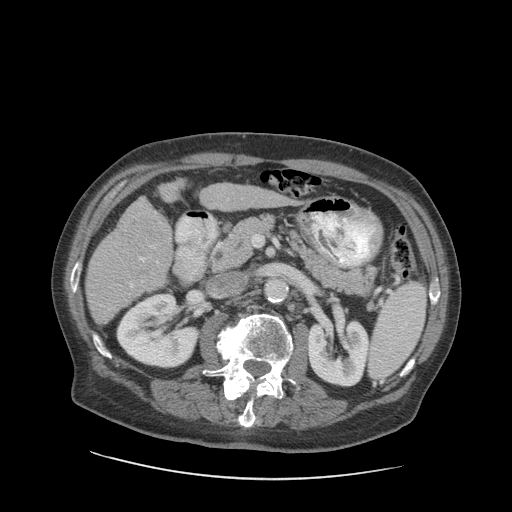
Contrast-enhanced abdominal CT (liver protocol), one axial slice. Slice 39 of 89 in the series (ordered by position). Soft-tissue window (W 400 / L 40 HU). 2.5 mm slice thickness. 512 × 512 image matrix, field of view 420 × 420 mm. From the clinical record (not read from this slice): diagnosis: hepatocellular carcinoma (patient treated with transarterial chemoembolisation; whether this scan precedes or follows treatment is not stated here); TNM stage (as recorded): Stage-I; Child-Pugh class: A; tumour differentiation: moderately differentiated; tumour nodularity: uninodular.
Outlined on this slice (semi-automatically segmented with operator editing):
- liver parenchyma outside the tumour (the mass and vessels are separate outlines, so this box may not span the whole liver): bounding box <86,186,286,324> (left, top, right, bottom; pixels)
- mass: <126,209,168,277>
- liver vessels: <101,205,159,310>